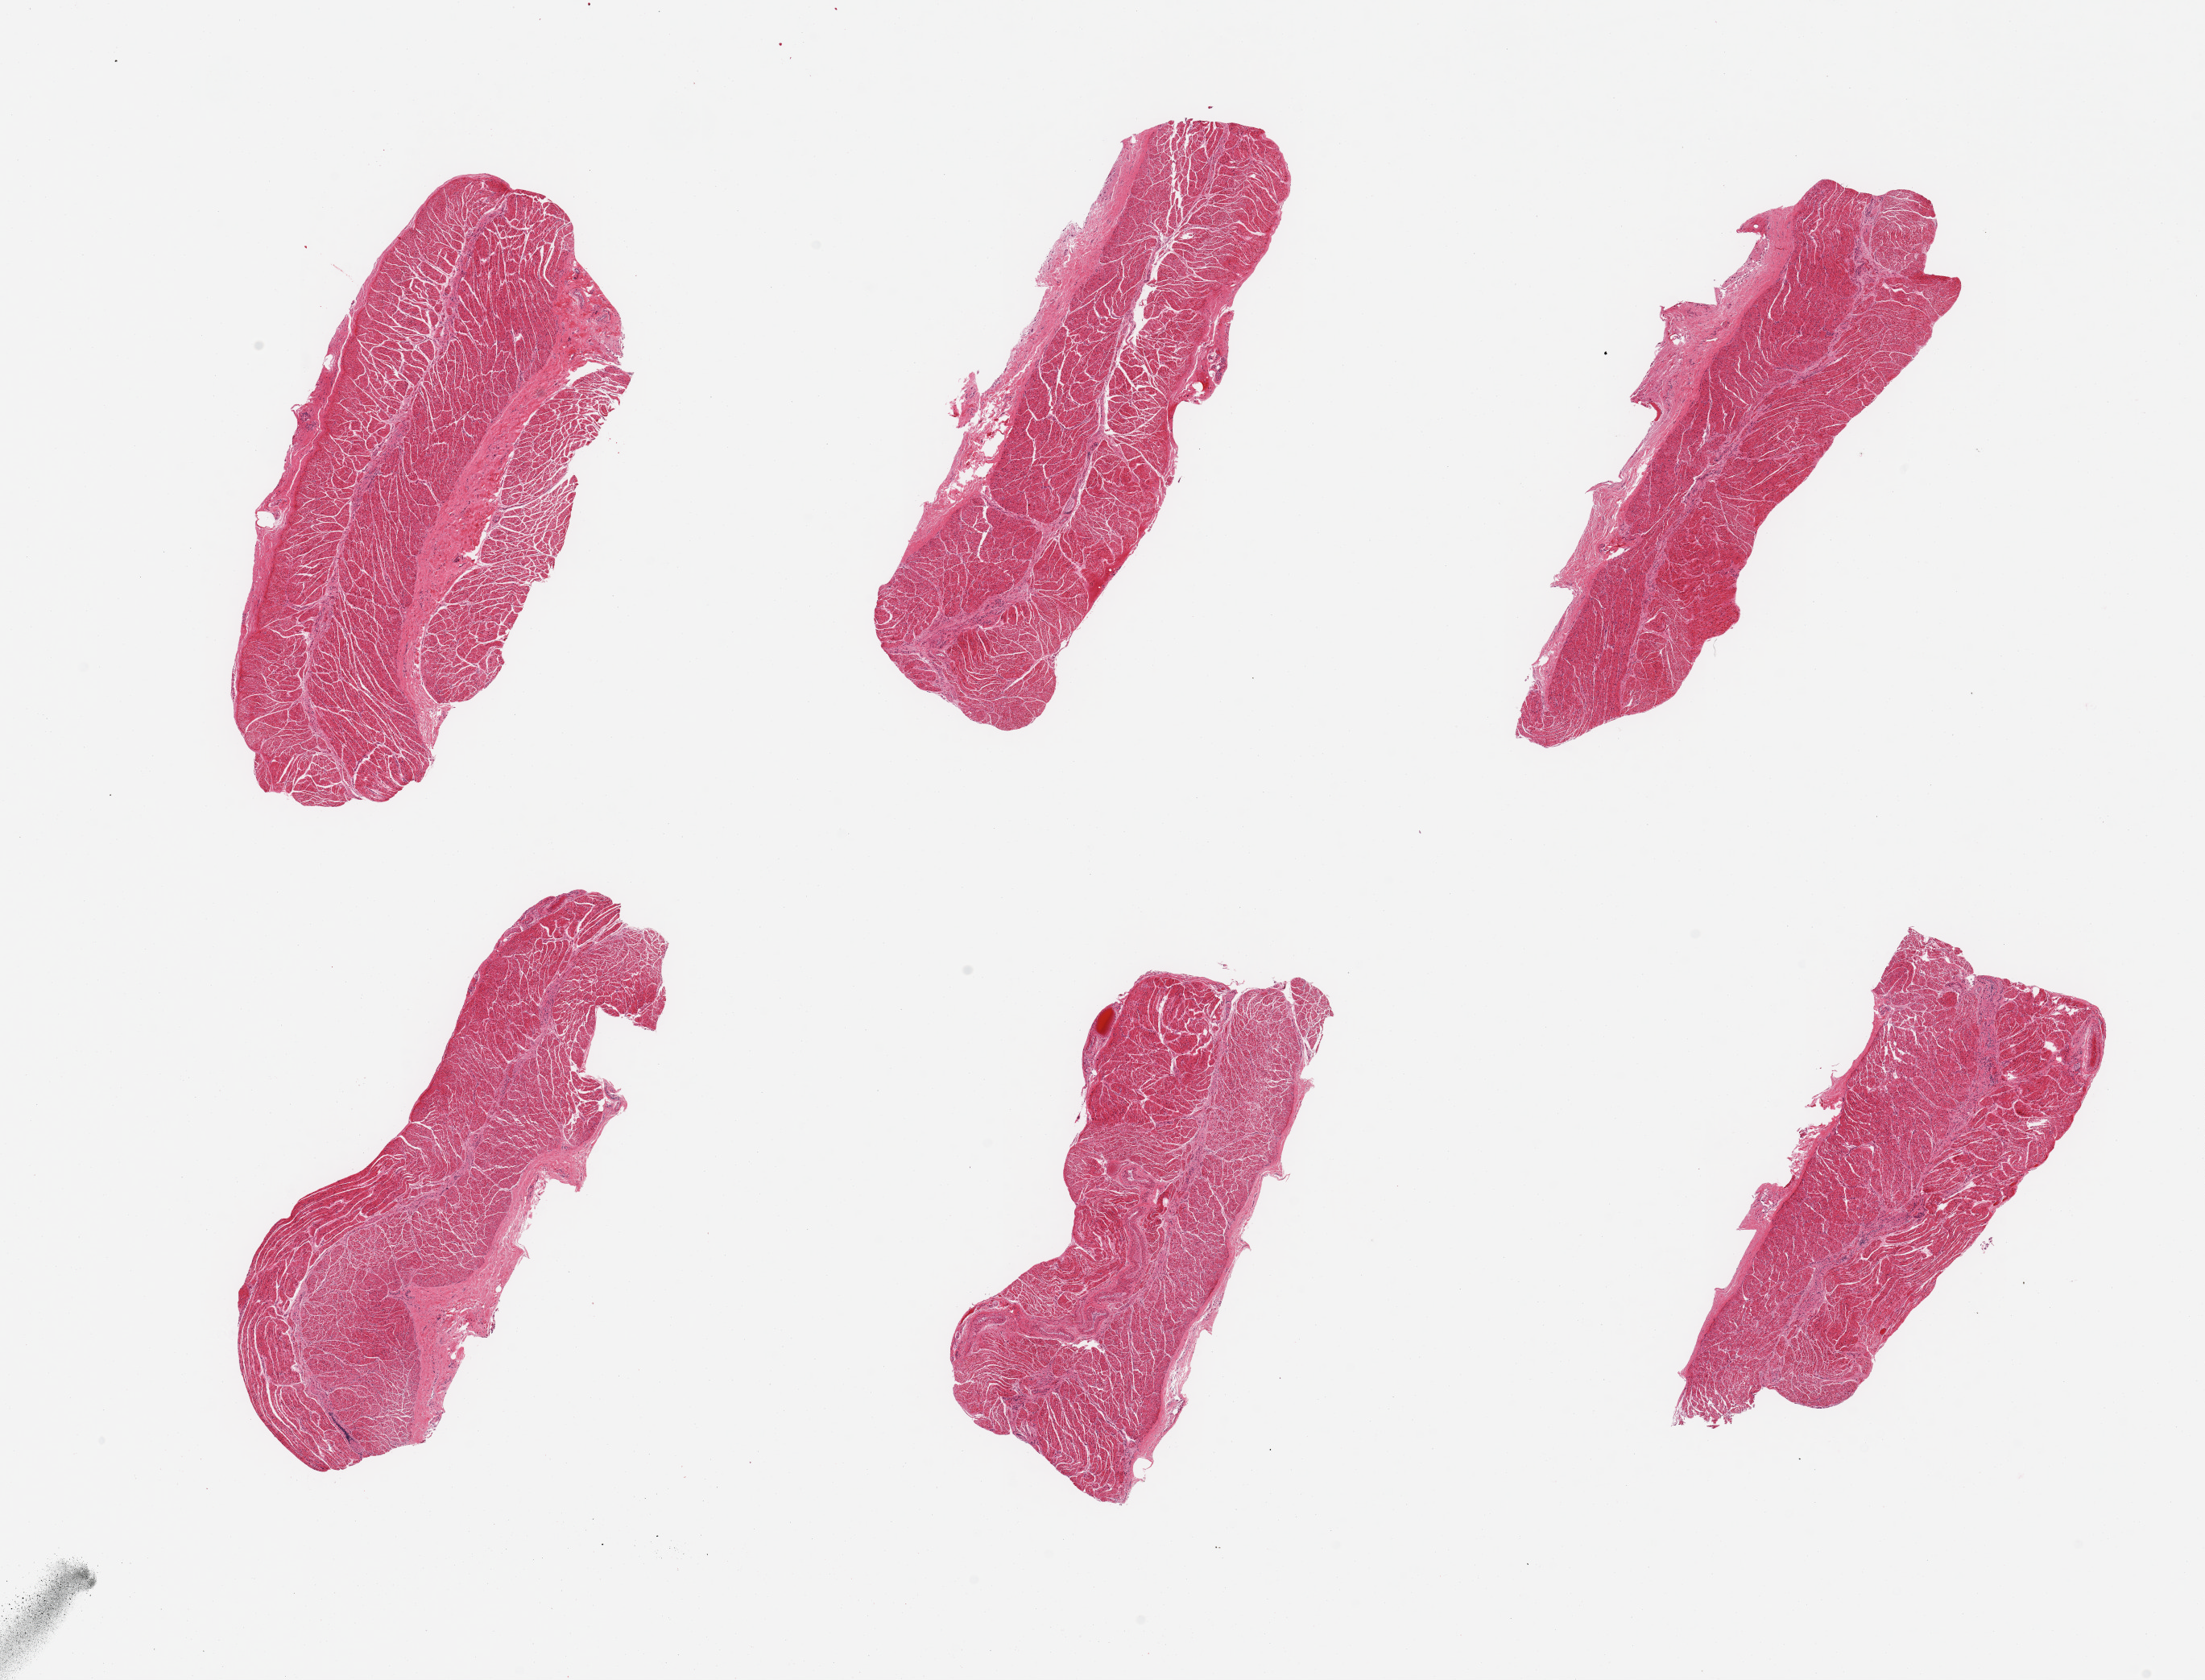
H&E whole-slide image — shown as a low-resolution overview of the whole scanned area (about 21.7 x 16.5 mm, from a 20x scan); PAXgene-fixed, paraffin-embedded tissue; target tissue: esophageal muscle; tissue donor sample. Female donor.
• pathologist's review note for this sample: 6 pieces; muscle fibers fragmented; well dissected